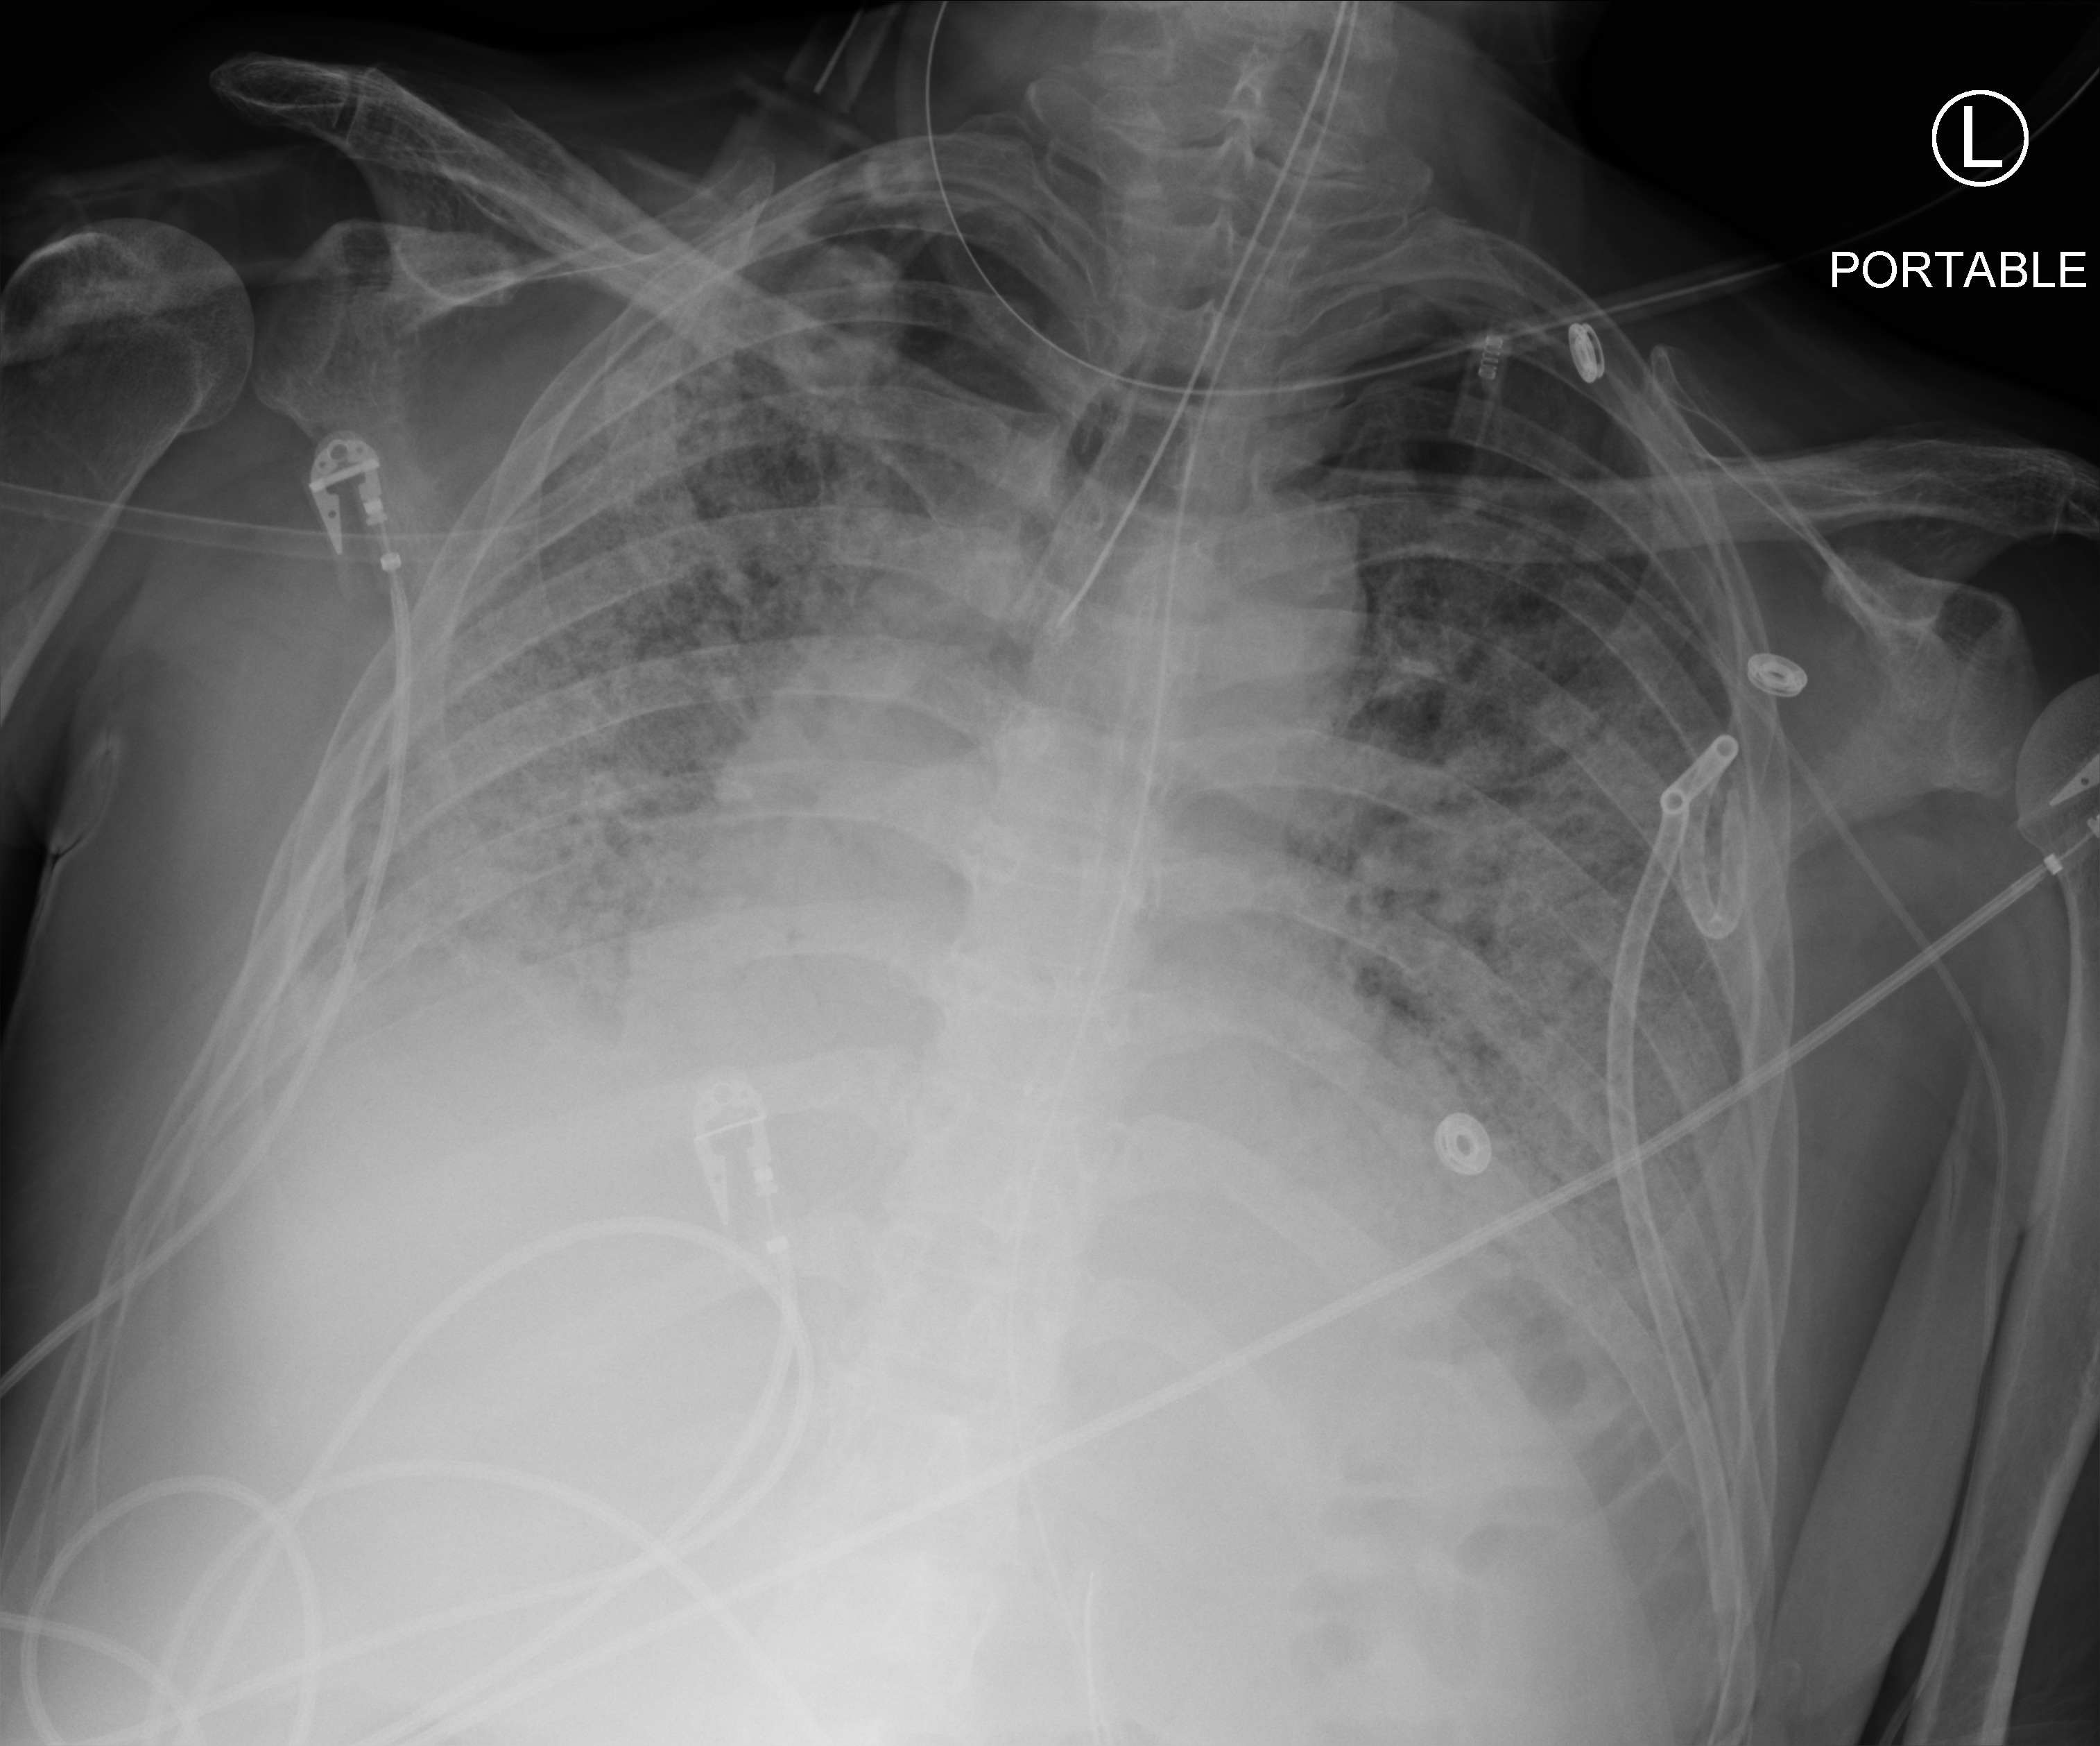
Portable chest radiograph; anteroposterior (AP) projection. Patient hospitalised with COVID-19; male, aged 60–74 years.
Admission-level facts for this patient (not findings on this image; timing relative to this image not recorded):
- mechanically ventilated during this hospital stay: yes
- admitted to intensive care during this hospital stay: yes